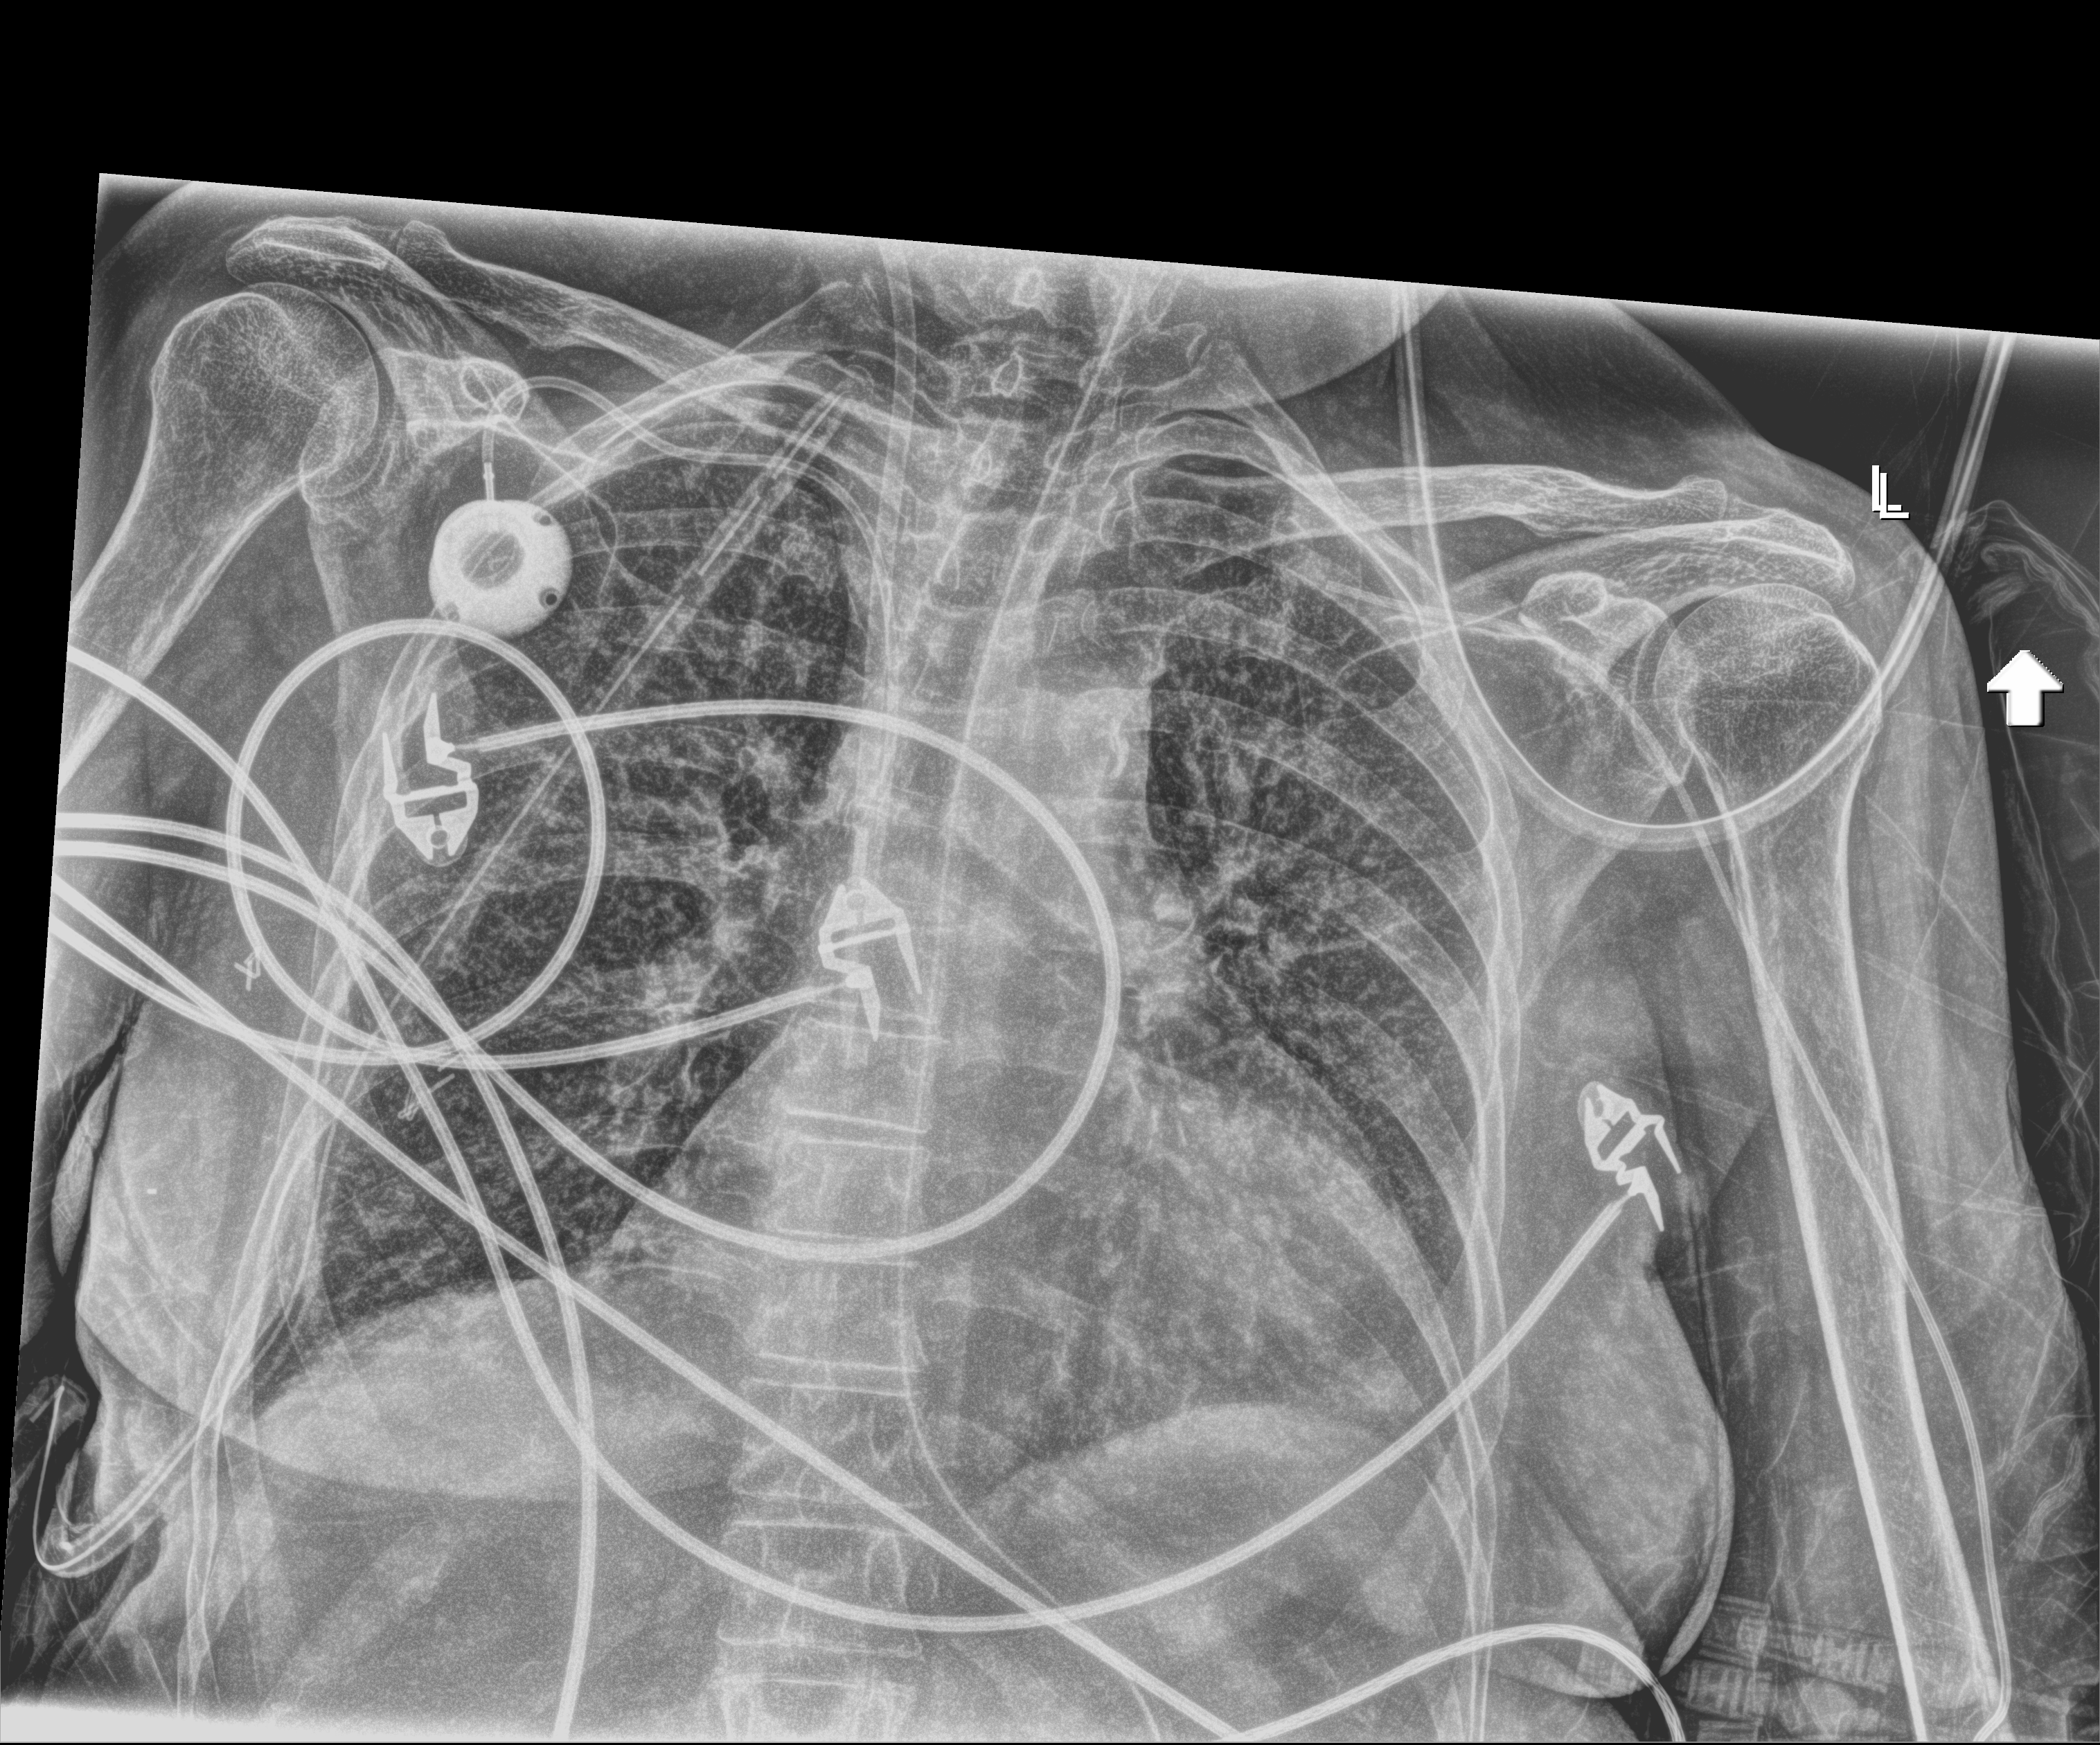
Chest radiograph; anteroposterior (AP) projection. Female patient hospitalised with COVID-19, age 60–74 years.
Admission-level facts for this patient (not findings on this image; timing relative to this image not recorded): mechanically ventilated during this hospital stay: yes.